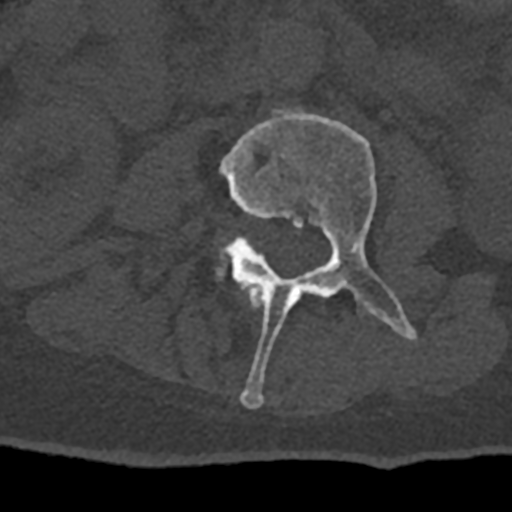
CT including the spine, one axial slice; position 315 of 797 along the scan axis; reconstruction kernel Br40s/3; 120 kVp; bone window (W 1800 / L 400 HU); 0.5 mm slice thickness; 512 × 512 image matrix, field of view 160 × 160 mm. Male patient, age 74 years. Case-level facts recorded for this patient, not image findings: primary cancer: renal.
Annotated regions visible in this slice (semi-automatically segmented with operator editing):
- L2 vertebra: bounding box <247,288,262,308> (left, top, right, bottom; pixels)
- L3 vertebra: <220,109,417,408>
- L4 vertebra: <220,251,226,272>